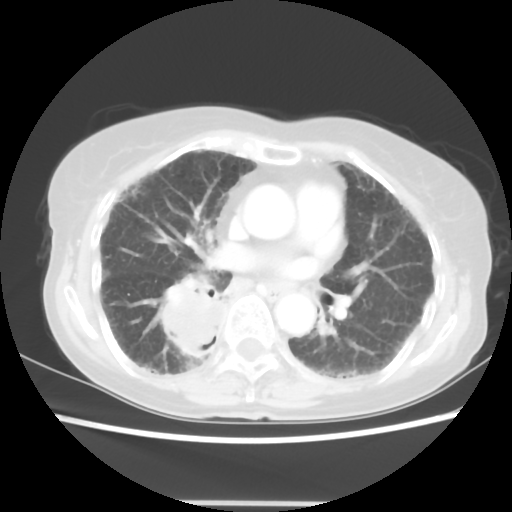
Chest CT, one axial slice. Position 27 of 52 along the scan axis. Lung window (W 1500 / L -600 HU). 5 mm slice thickness. 512 × 512 image matrix, field of view 325 × 325 mm. Patient: female, 71 years. From the clinical record (not read from this slice): clinical TNM (as recorded): T3 N0 M0.
Structures marked on this image (bounding box drawn by a radiologist):
- lung tumour (recorded histology: squamous cell carcinoma): bounding box <159,286,228,362> (left, top, right, bottom; pixels)